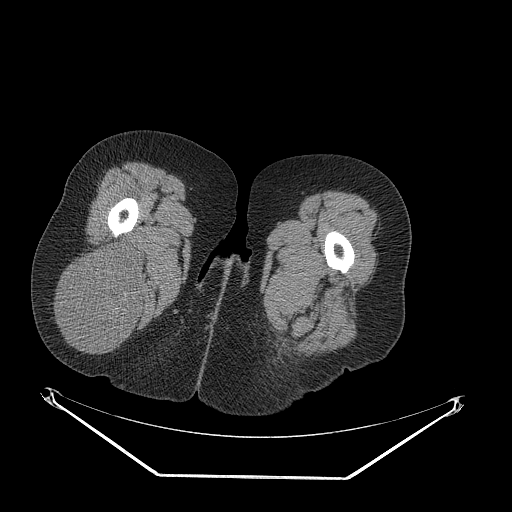
CT of an extremity soft-tissue mass (from a PET/CT study), one axial slice; position 43 of 257 along the scan axis; reconstruction kernel STANDARD; soft-tissue window (W 400 / L 40 HU); 3.75 mm slice thickness; 512 × 512 image matrix. Female patient. Case-level facts recorded for this patient, not image findings: histological type: synovial sarcoma; grade: intermediate; site of the primary tumour: right buttock.
Outlined on this slice (expert contour drawn on MRI and transferred to this co-registered scan by the dataset authors):
- gross tumour volume including surrounding oedema: box from (x=62, y=246) to (x=147, y=348) px
- gross tumour volume (mass): (x=62, y=246)–(x=147, y=348)